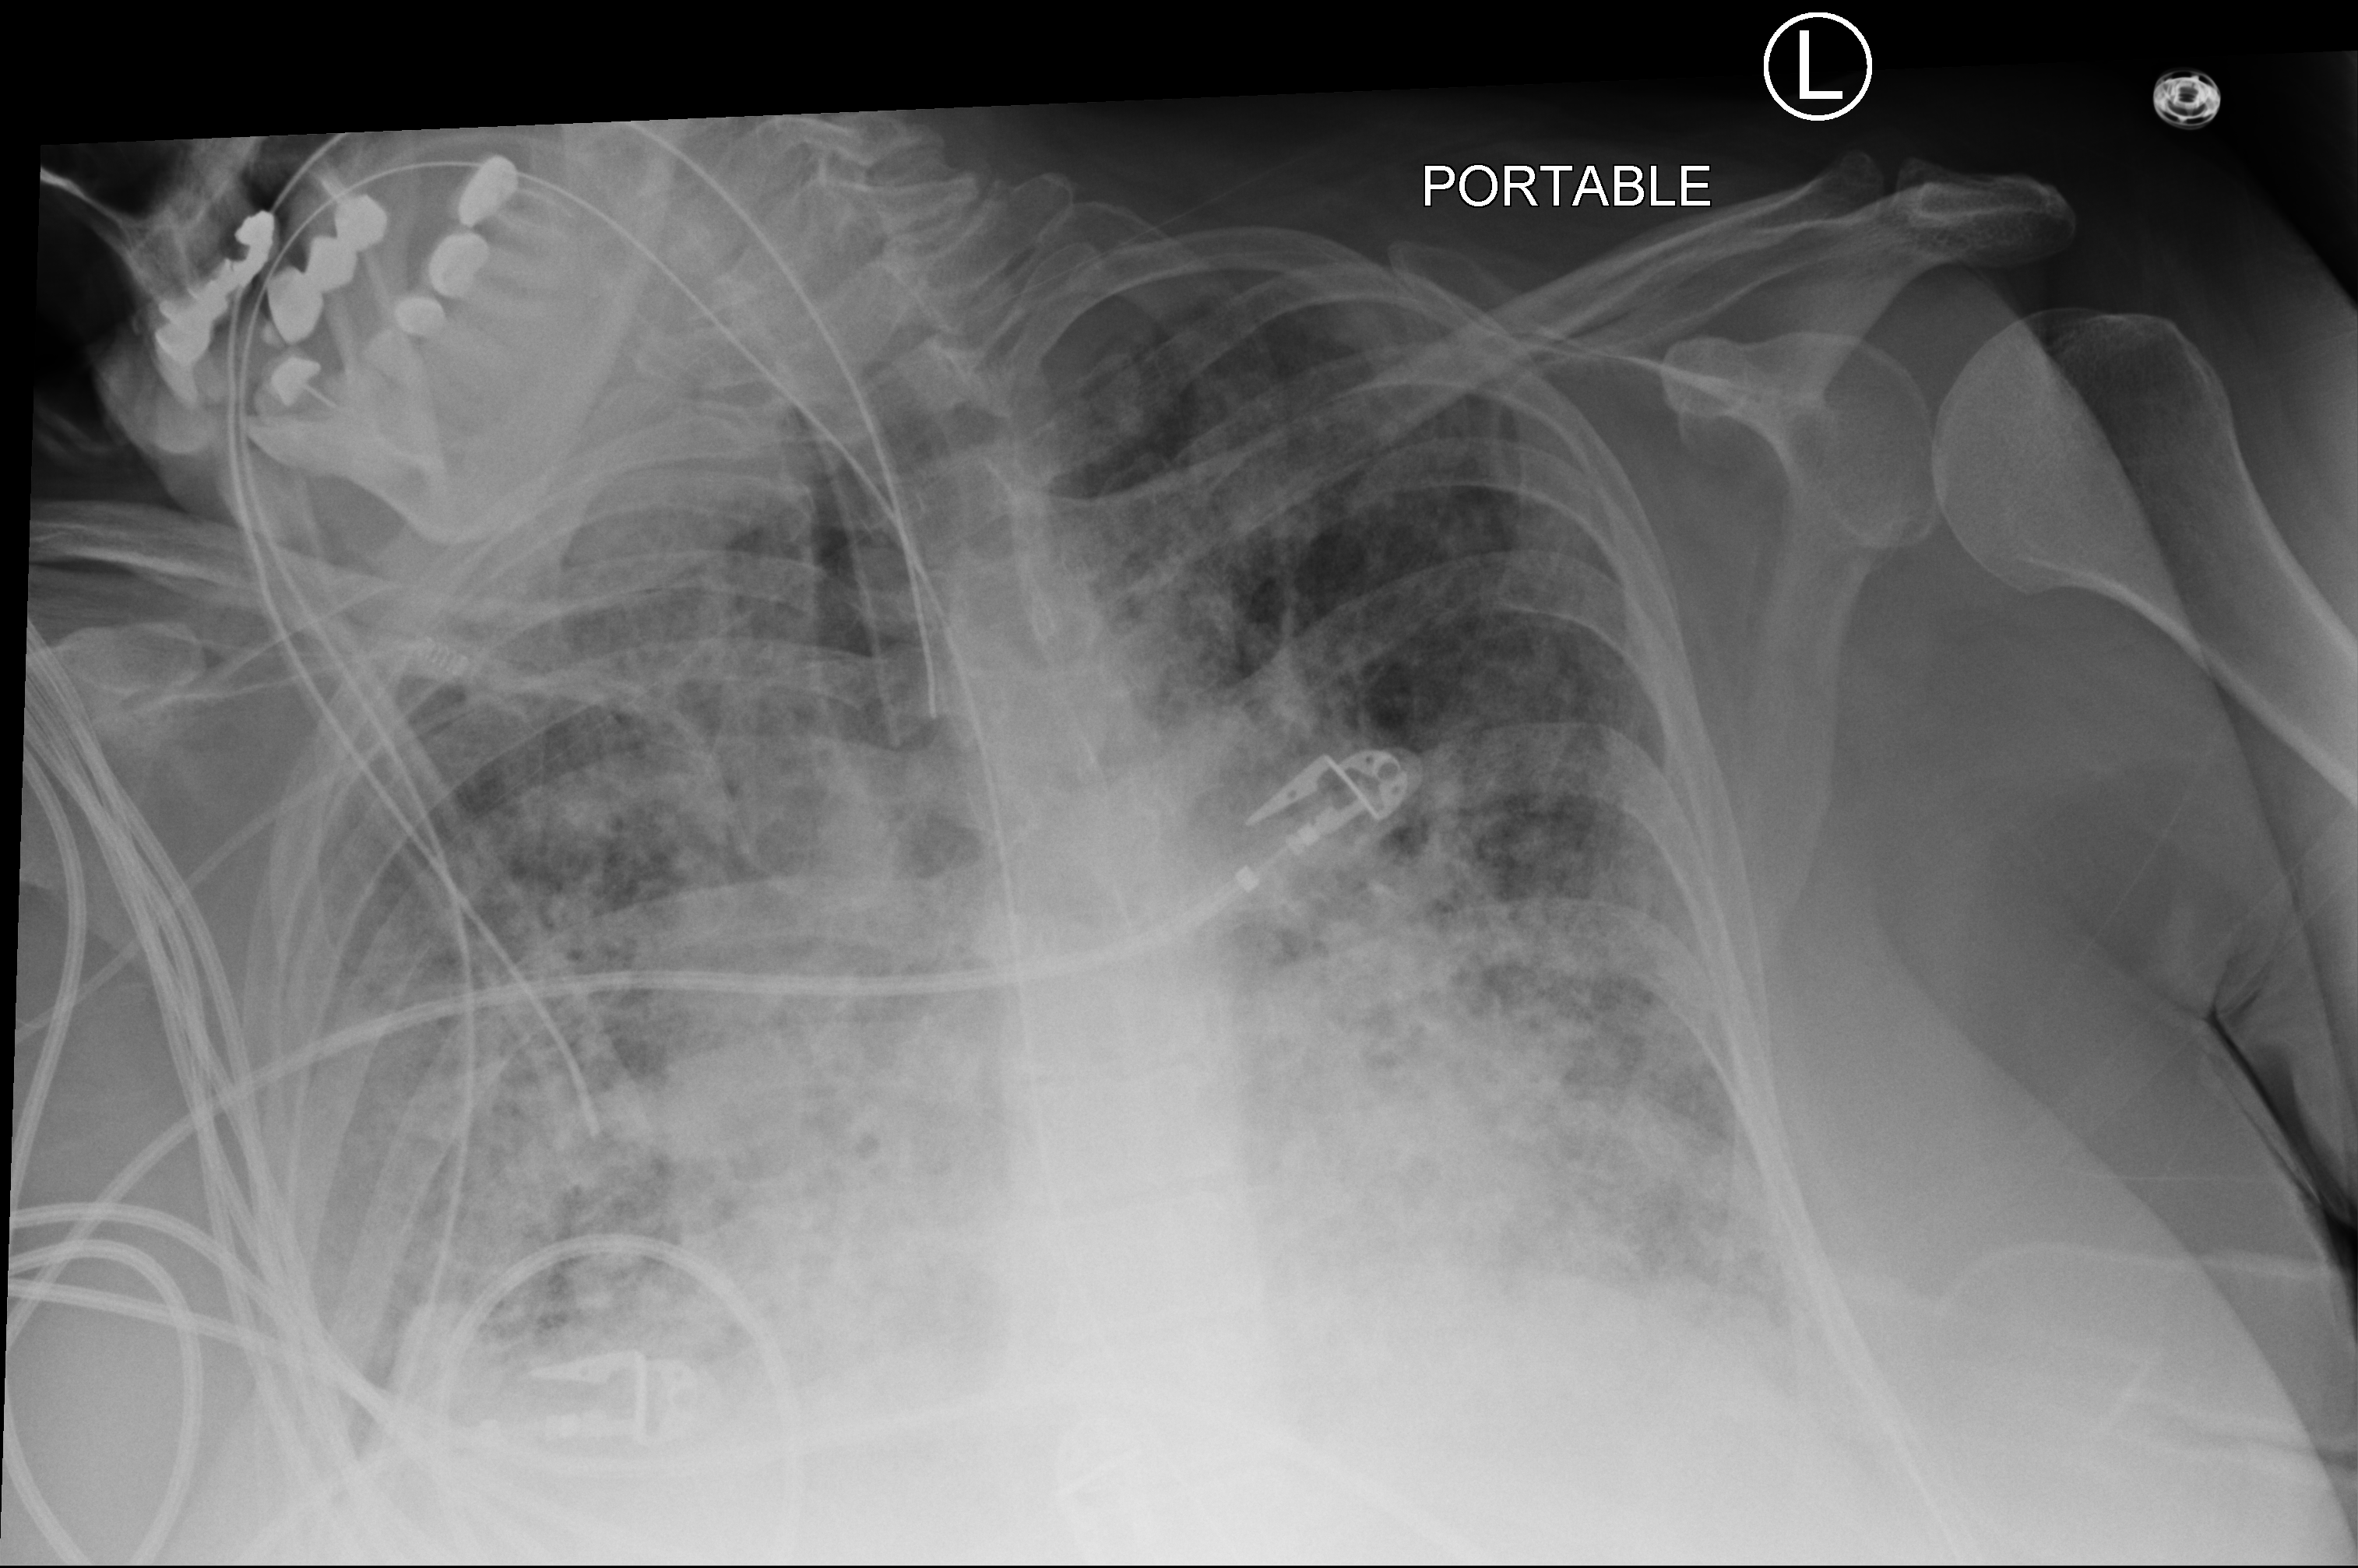
Portable chest radiograph, anteroposterior (AP) projection. Patient hospitalised with COVID-19; female, aged 60–74 years.
From the hospital-stay record, not from the radiograph (when in the stay this image was taken is not recorded):
- admitted to intensive care during this hospital stay: yes
- mechanically ventilated during this hospital stay: yes